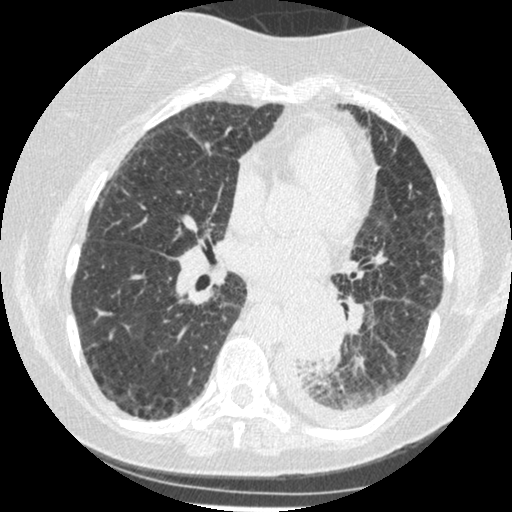
Axial slice from a low-dose chest CT screening exam. Third annual screen. Lung window (W 1500 / L -600 HU). Slice 230 of 341 in the series. 512 × 512 image matrix. Female participant, aged 60 years at enrolment. Former smoker at enrolment.
- Expert reader's lesion annotation, box from (x=275, y=304) to (x=343, y=375) px.
- The exam's reader record, not a measurement of the box and not confirmed to be the same lesion: non-calcified nodule or mass ≥4 mm, left lower lobe, 54 × 38 mm, smooth margins, soft tissue attenuation, pre-existing on the prior screen: yes; interval growth: yes.
- Later outcome: lung cancer diagnosed 15 days after this screen — small cell carcinoma, NOS, left lower lobe, undifferentiated (G4), stage IV (AJCC 6th edition), 69 mm at pathology.